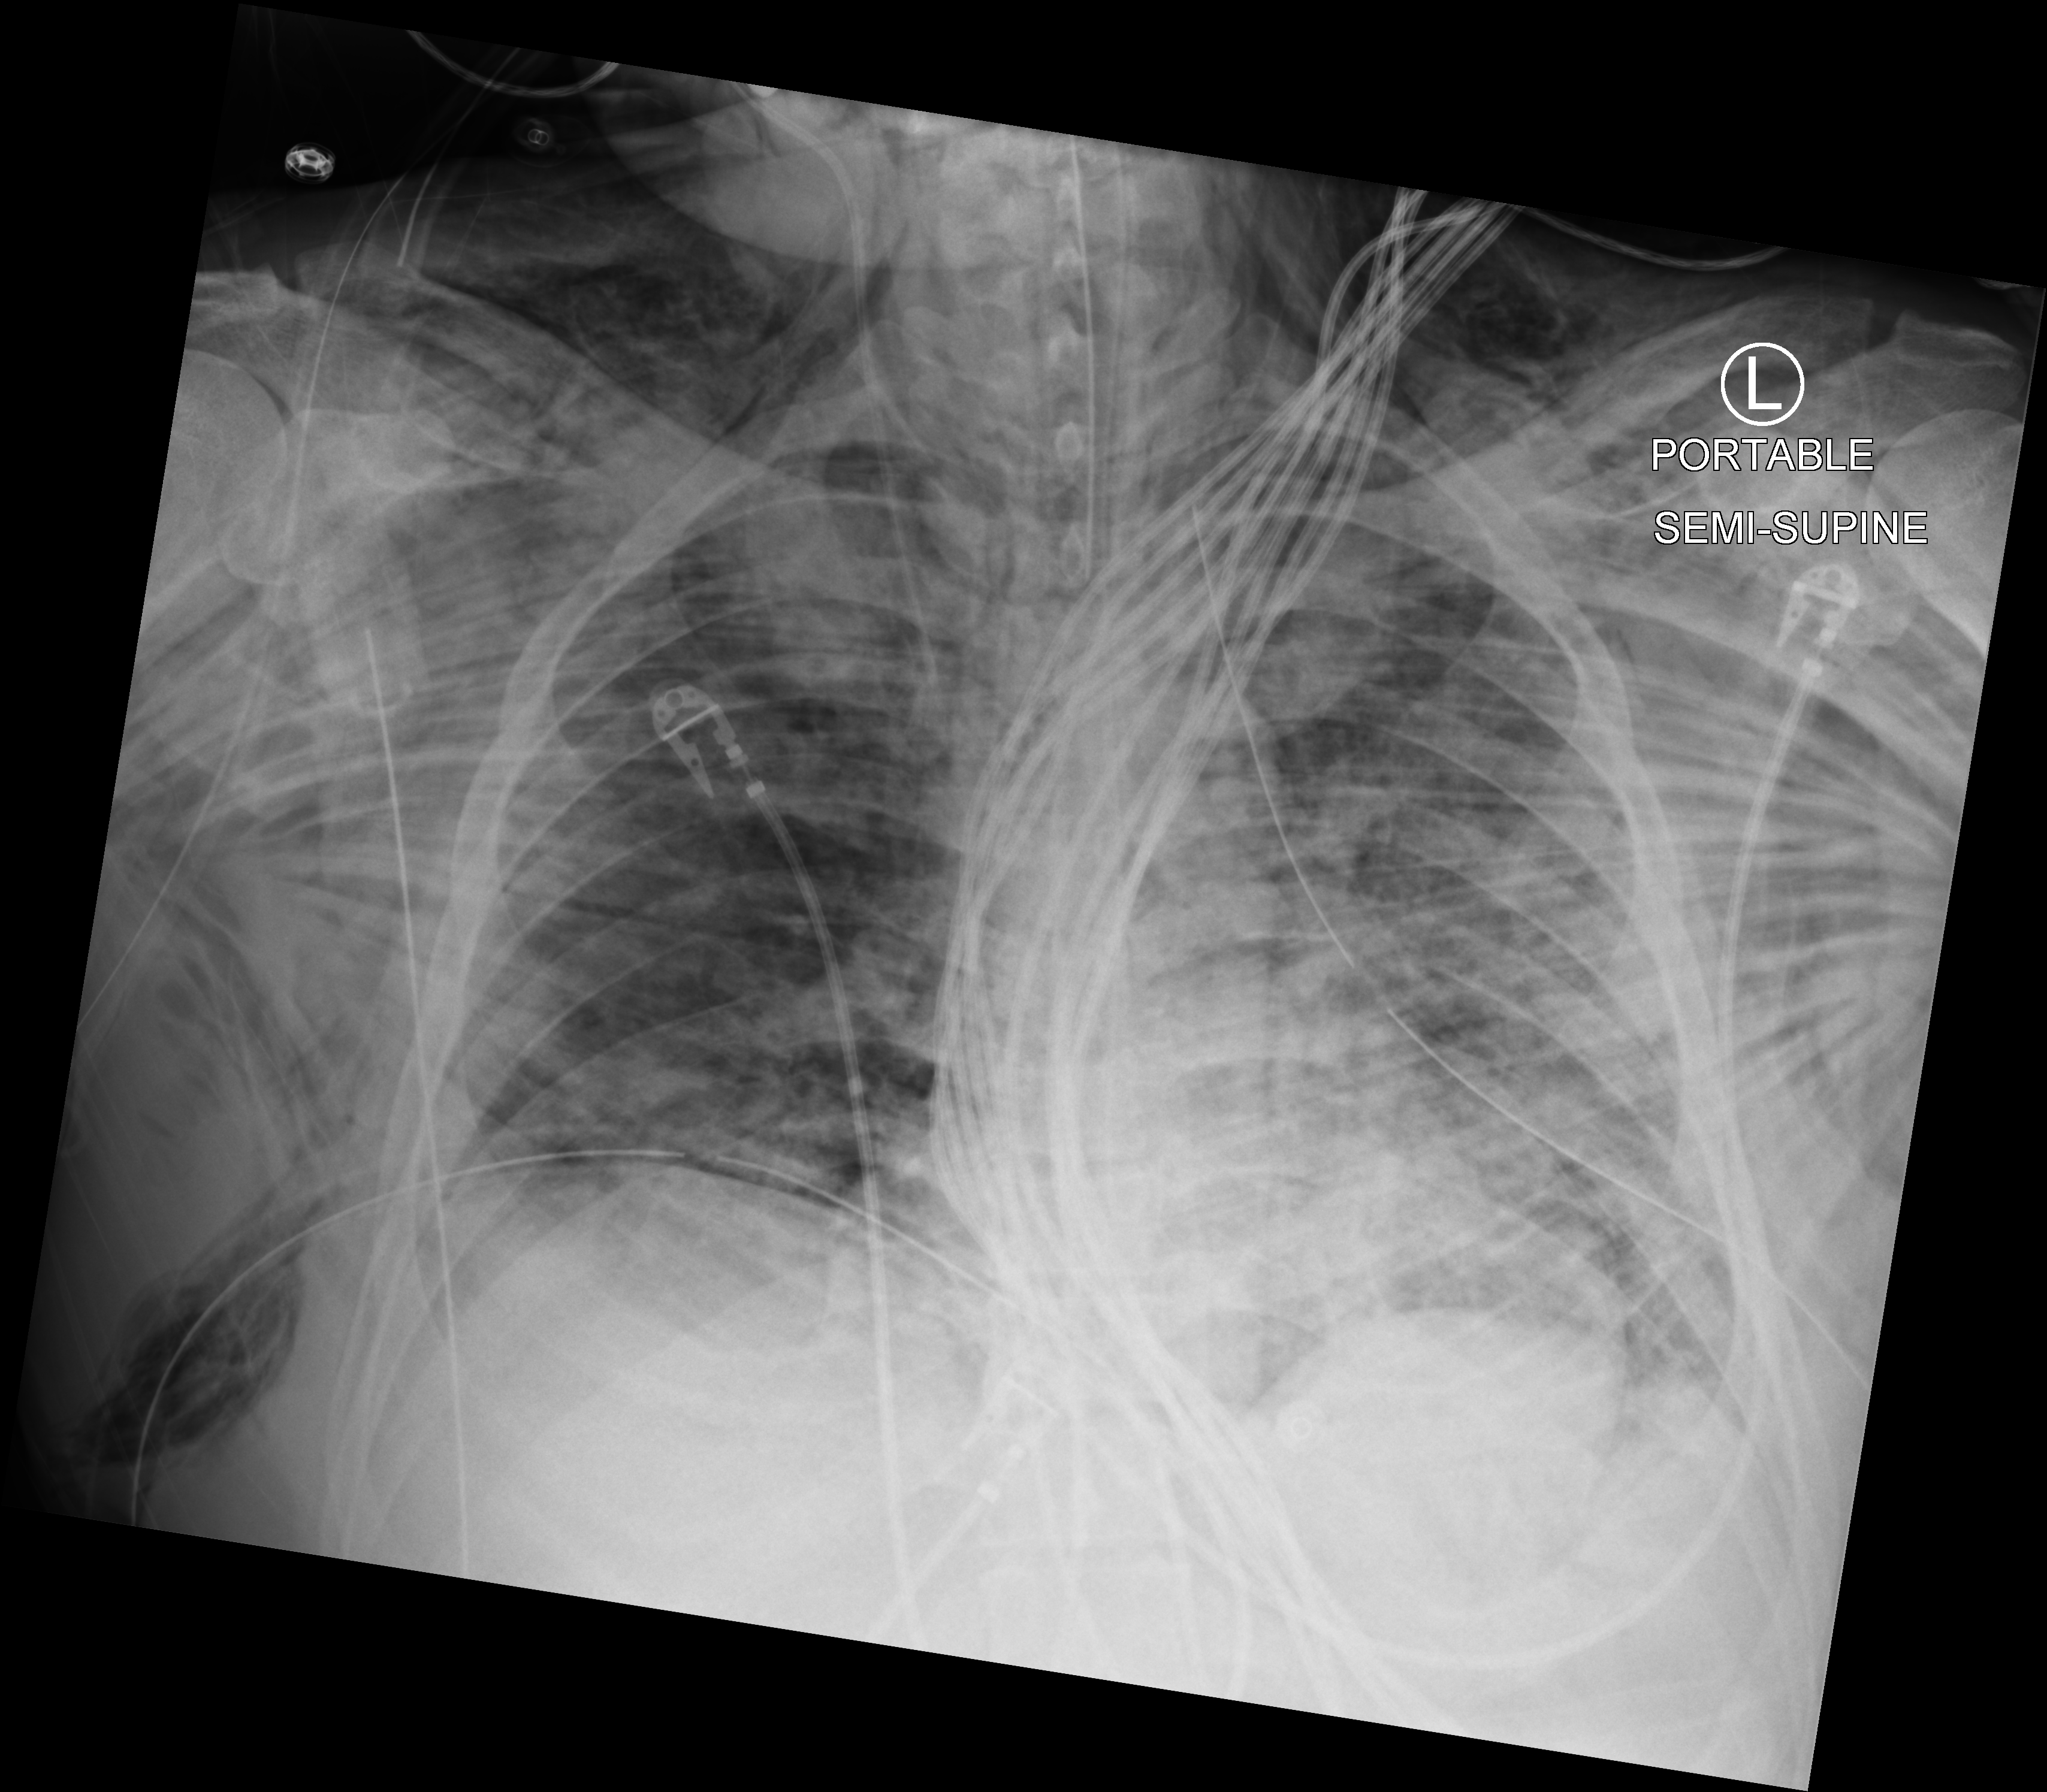
Portable chest radiograph, anteroposterior (AP) projection. Patient hospitalised with COVID-19; male, aged 18–59 years.
Admission-level facts for this patient (not findings on this image; timing relative to this image not recorded): mechanically ventilated during this hospital stay: yes.